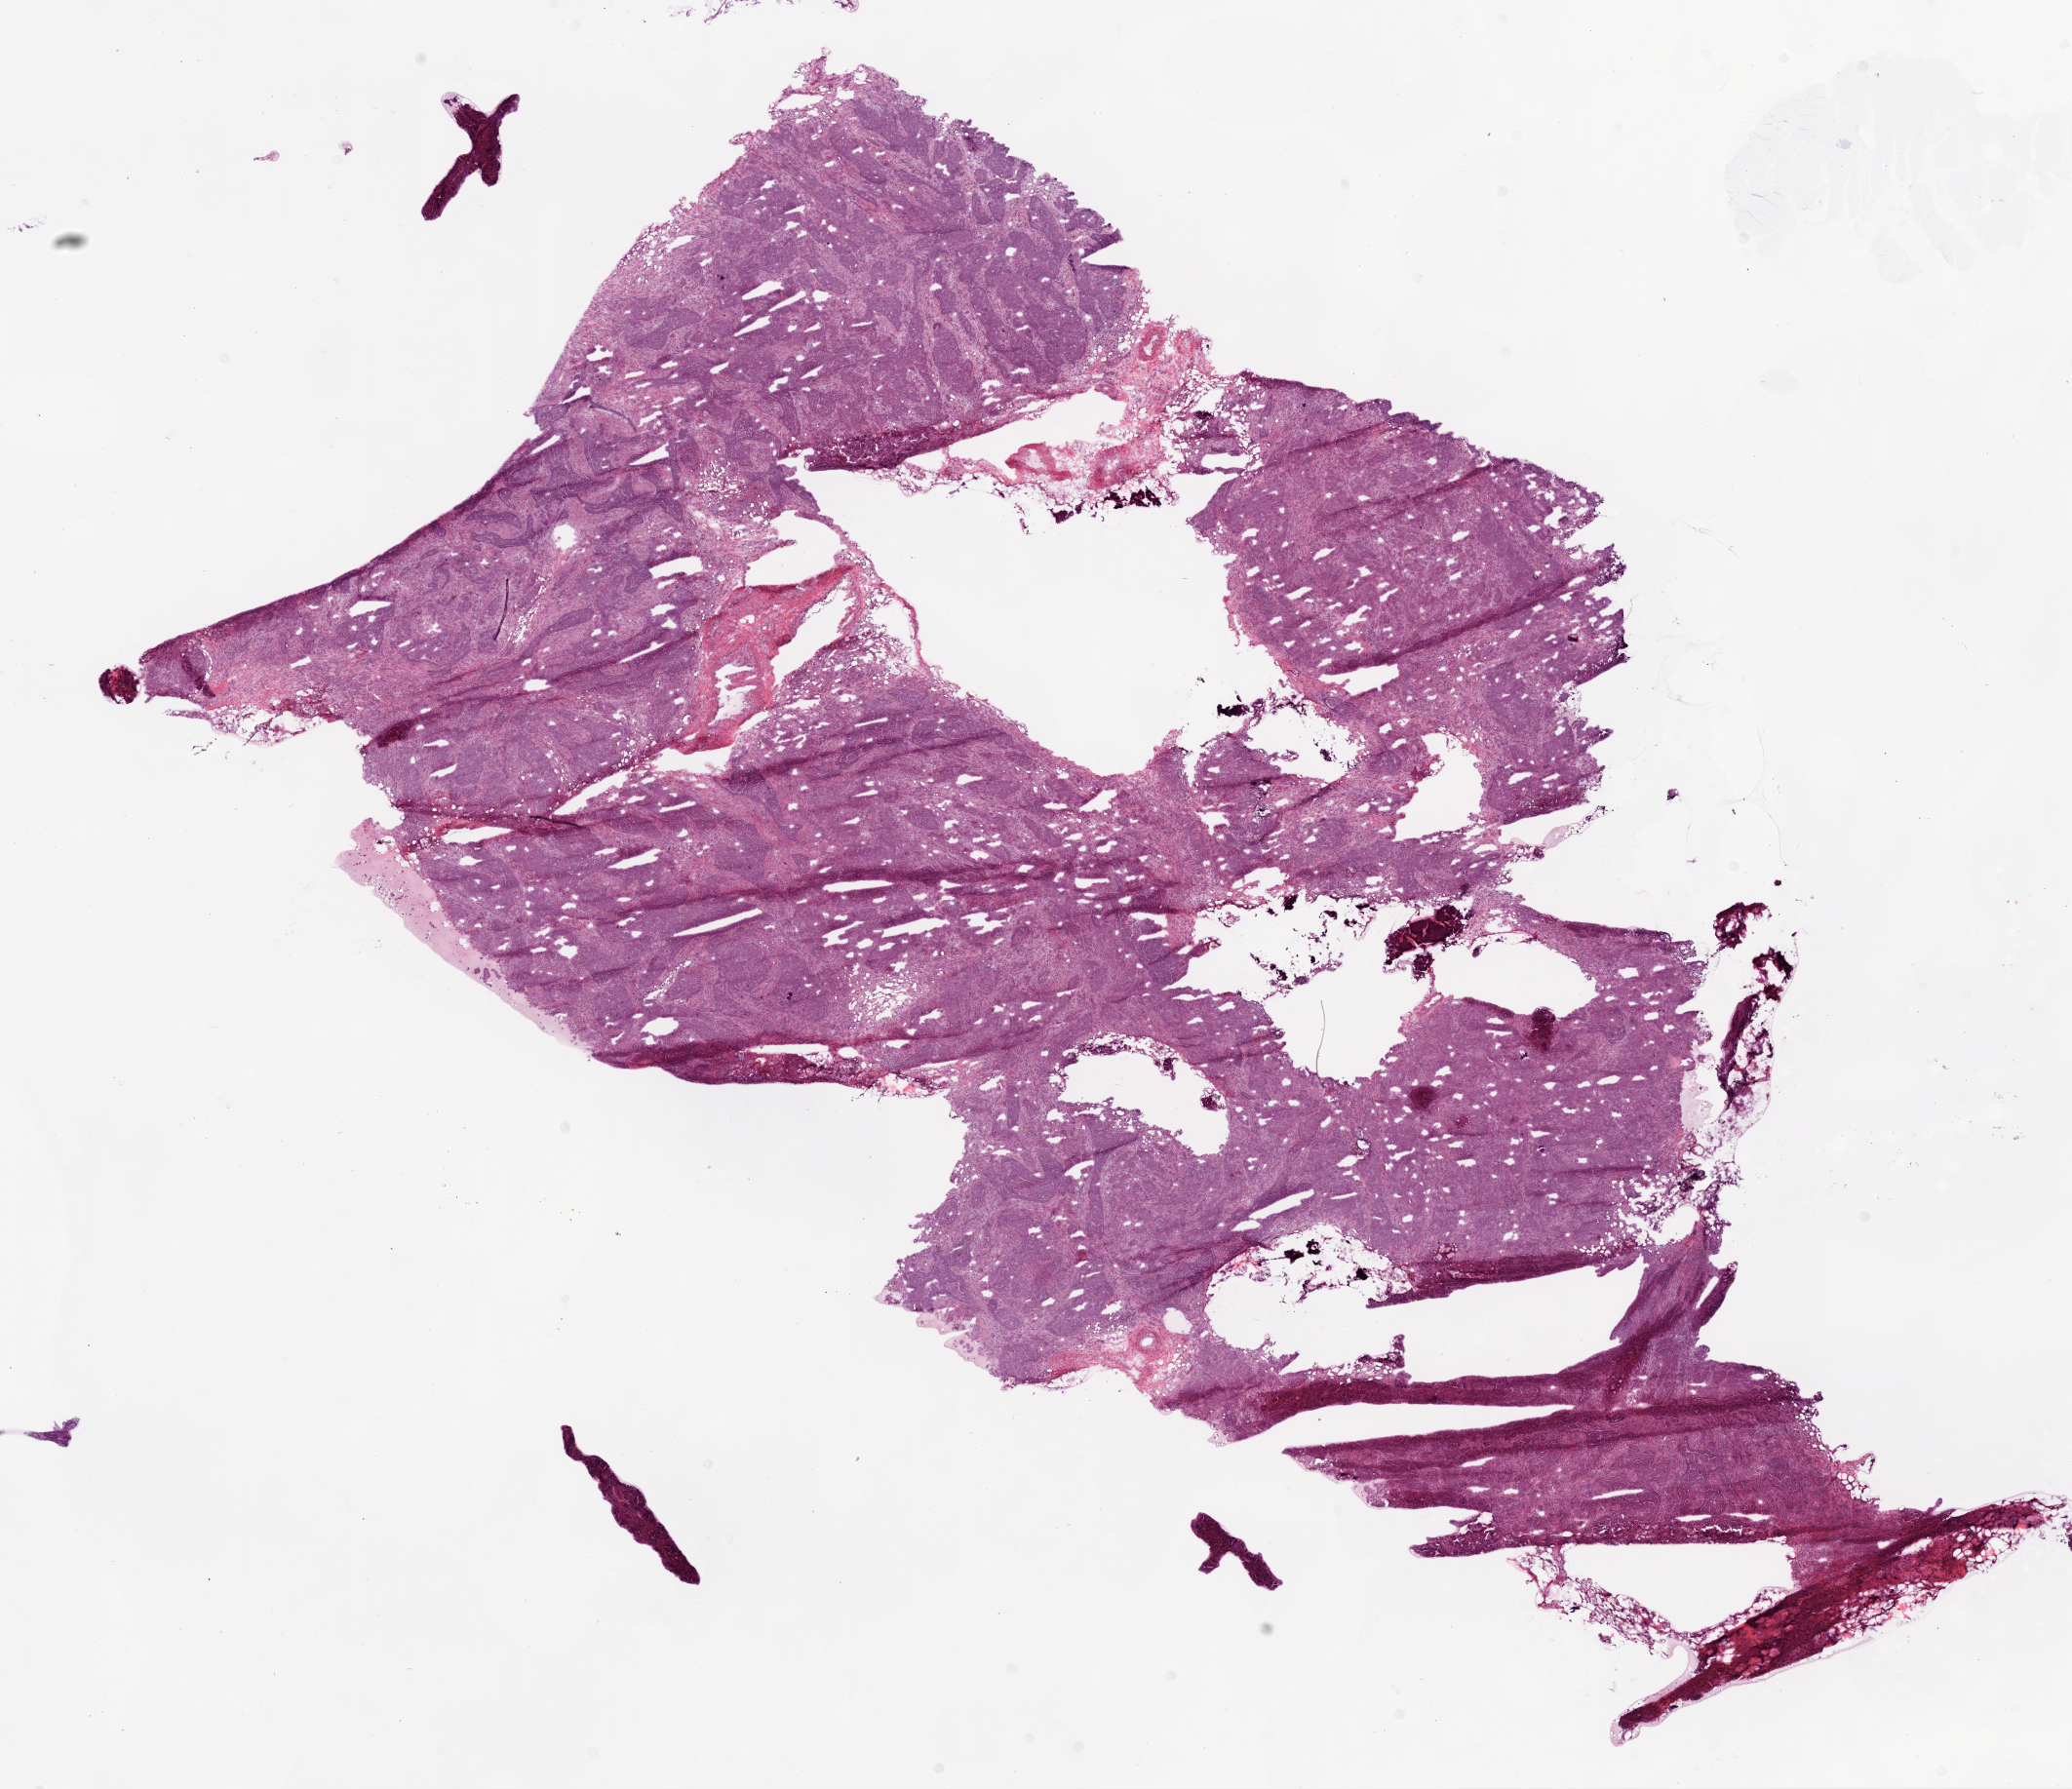
H&E whole-slide image — low-resolution overview of the scanned area, about 17.1 x 14.7 mm (from a 20x scan); frozen section from the bottom of the tissue portion; sample: primary tumour, ovary. Female, age 76 years at initial diagnosis. Histologic grade: G3 (poorly differentiated). Composition of this section per pathologist review: tumour cells 88%, tumour nuclei 95%, normal cells 0%, stromal cells 10%, necrosis 2%.
Histologic diagnosis: Serous cystadenocarcinoma, NOS. FIGO stage: IIIC.